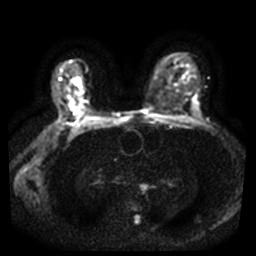
Breast MRI, one axial slice; slice 25 of 44 in the series (ordered by position); diffusion-weighted series; image 2 of 4 stored at this slice position (different b-values; order by instance number); 3 T; 5 mm slice thickness; 256 × 256 image matrix, field of view 340 × 340 mm. Female patient.
Annotated regions visible in this slice (manually delineated by an expert):
- tumour on diffusion-weighted imaging: bounding box [x1, y1, x2, y2] px = [67, 105, 77, 111]